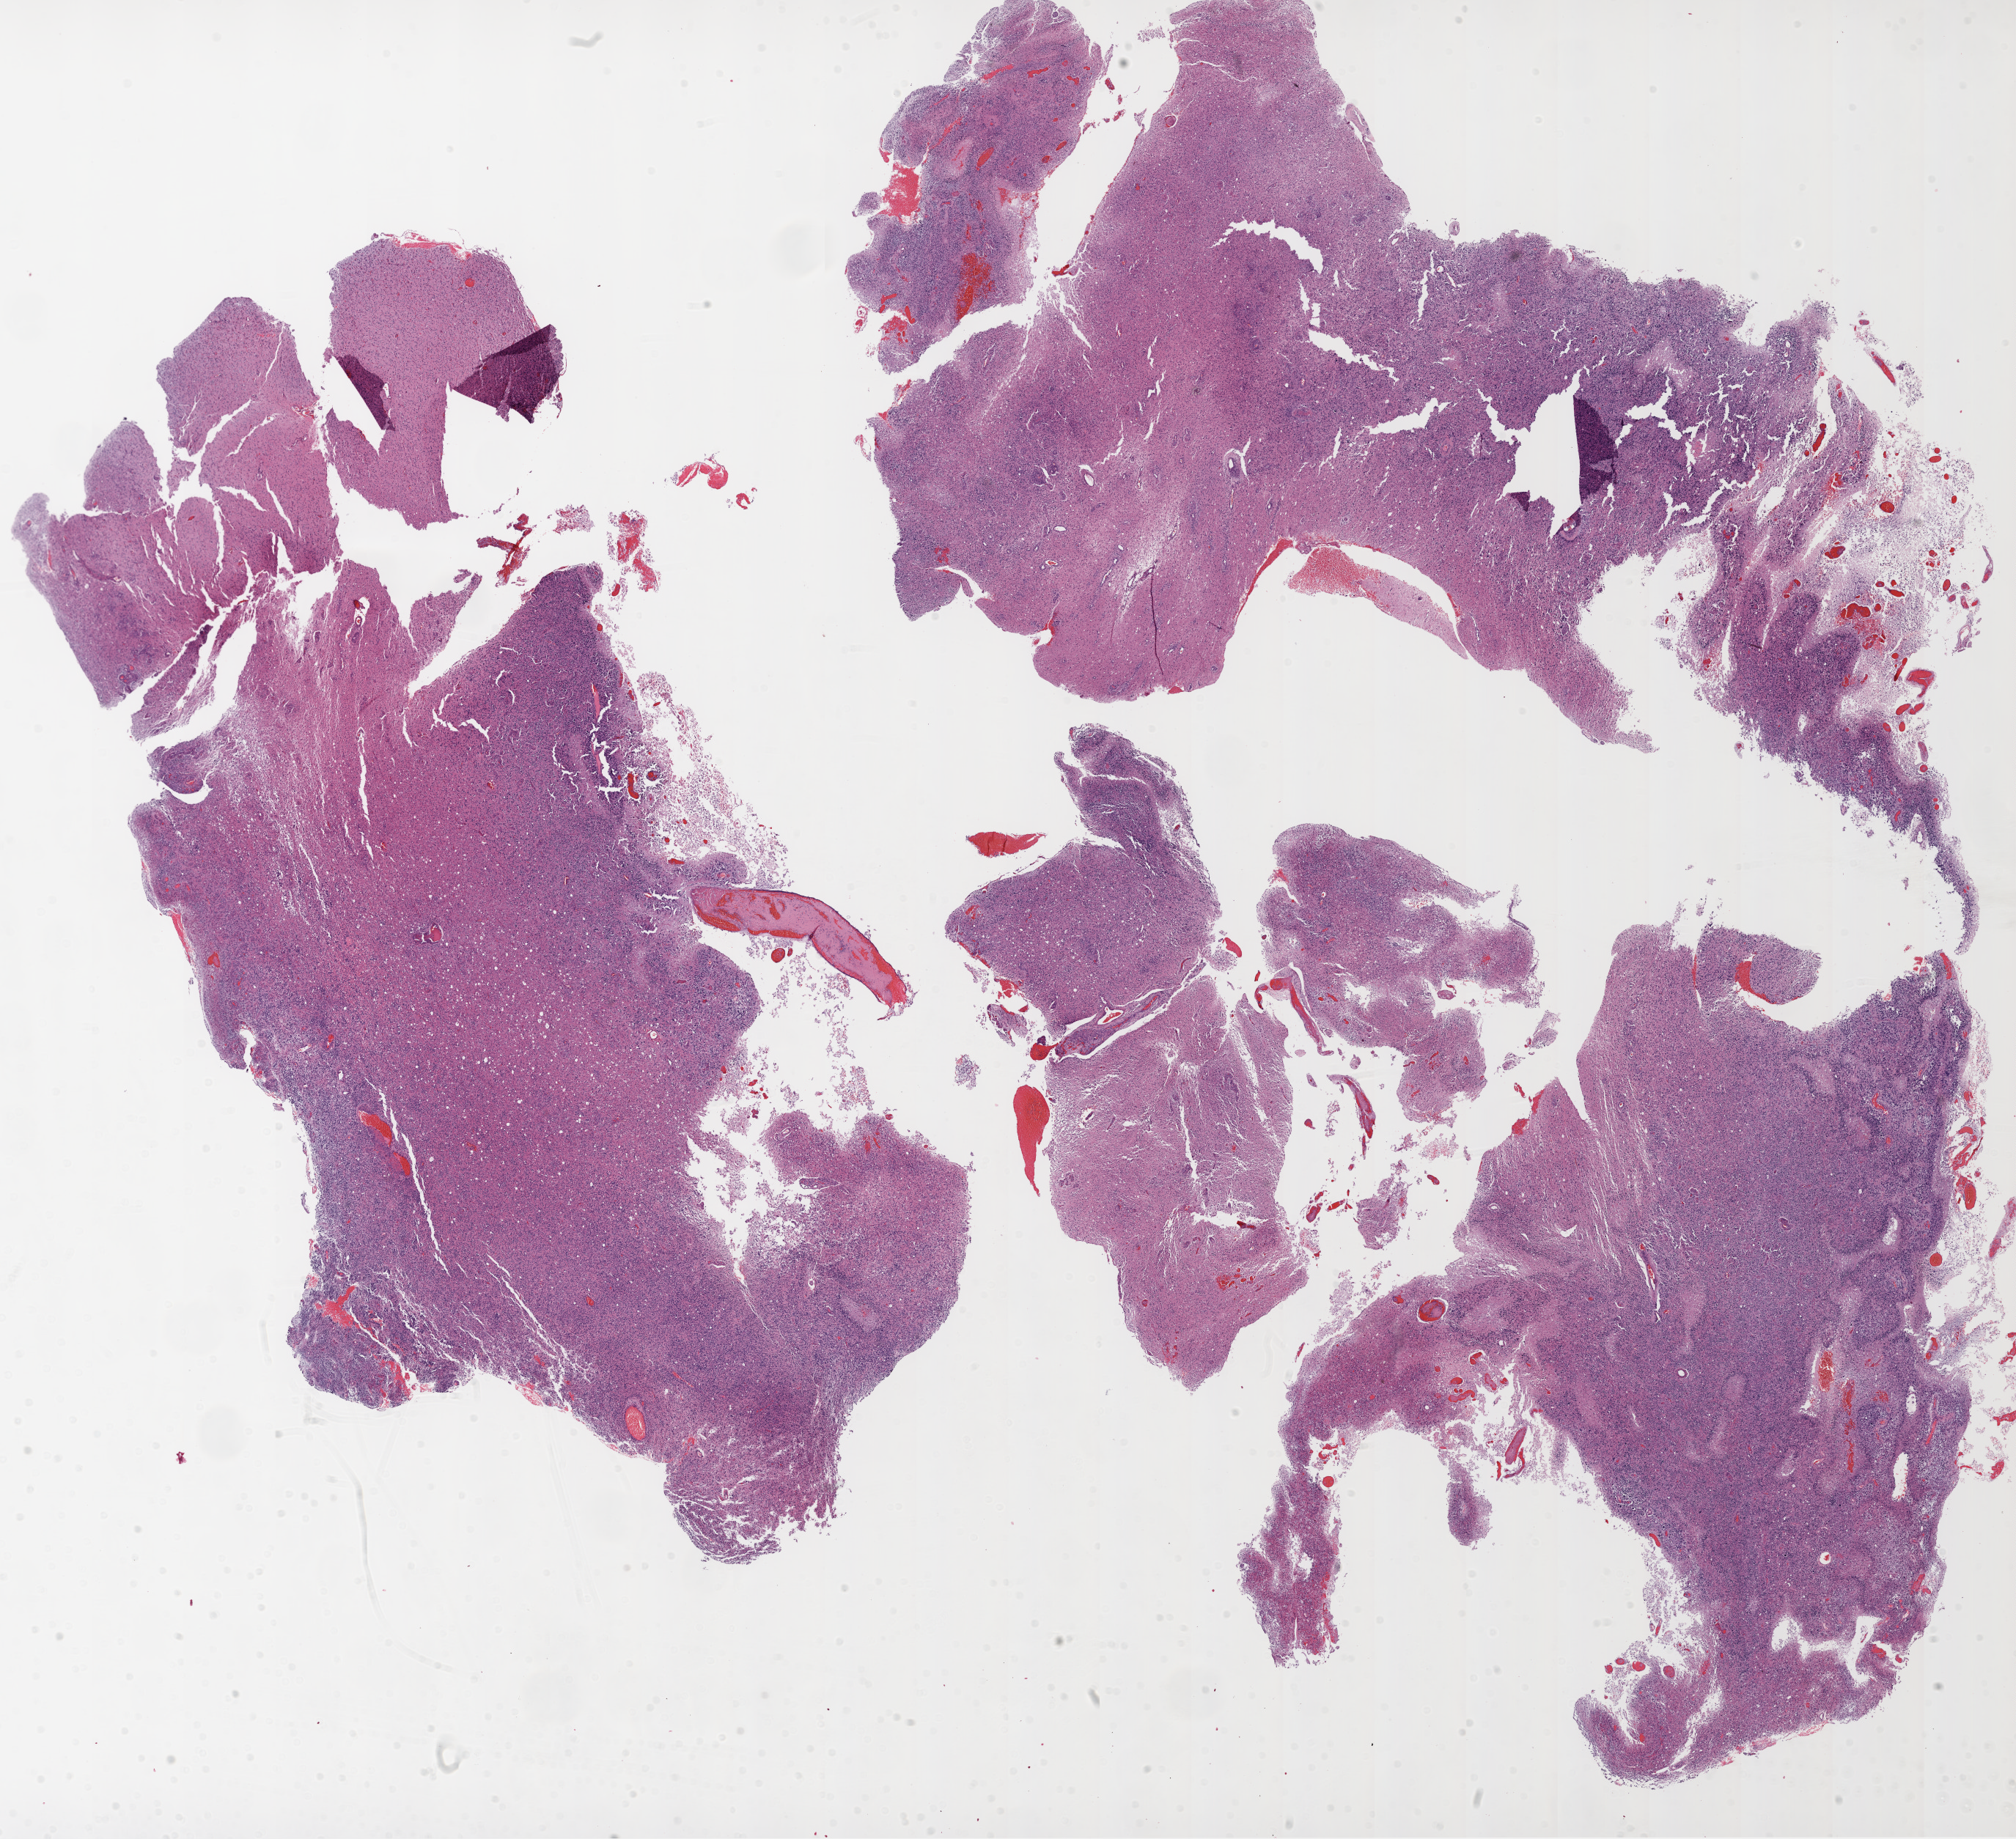
H&E whole-slide image, a low-resolution overview of the entire scanned area, about 22.1 x 20.1 mm; formalin-fixed paraffin-embedded (FFPE) diagnostic section; primary tumour sample from the brain. Patient: male, age at initial diagnosis 70 years.
Histologic diagnosis: Glioblastoma.